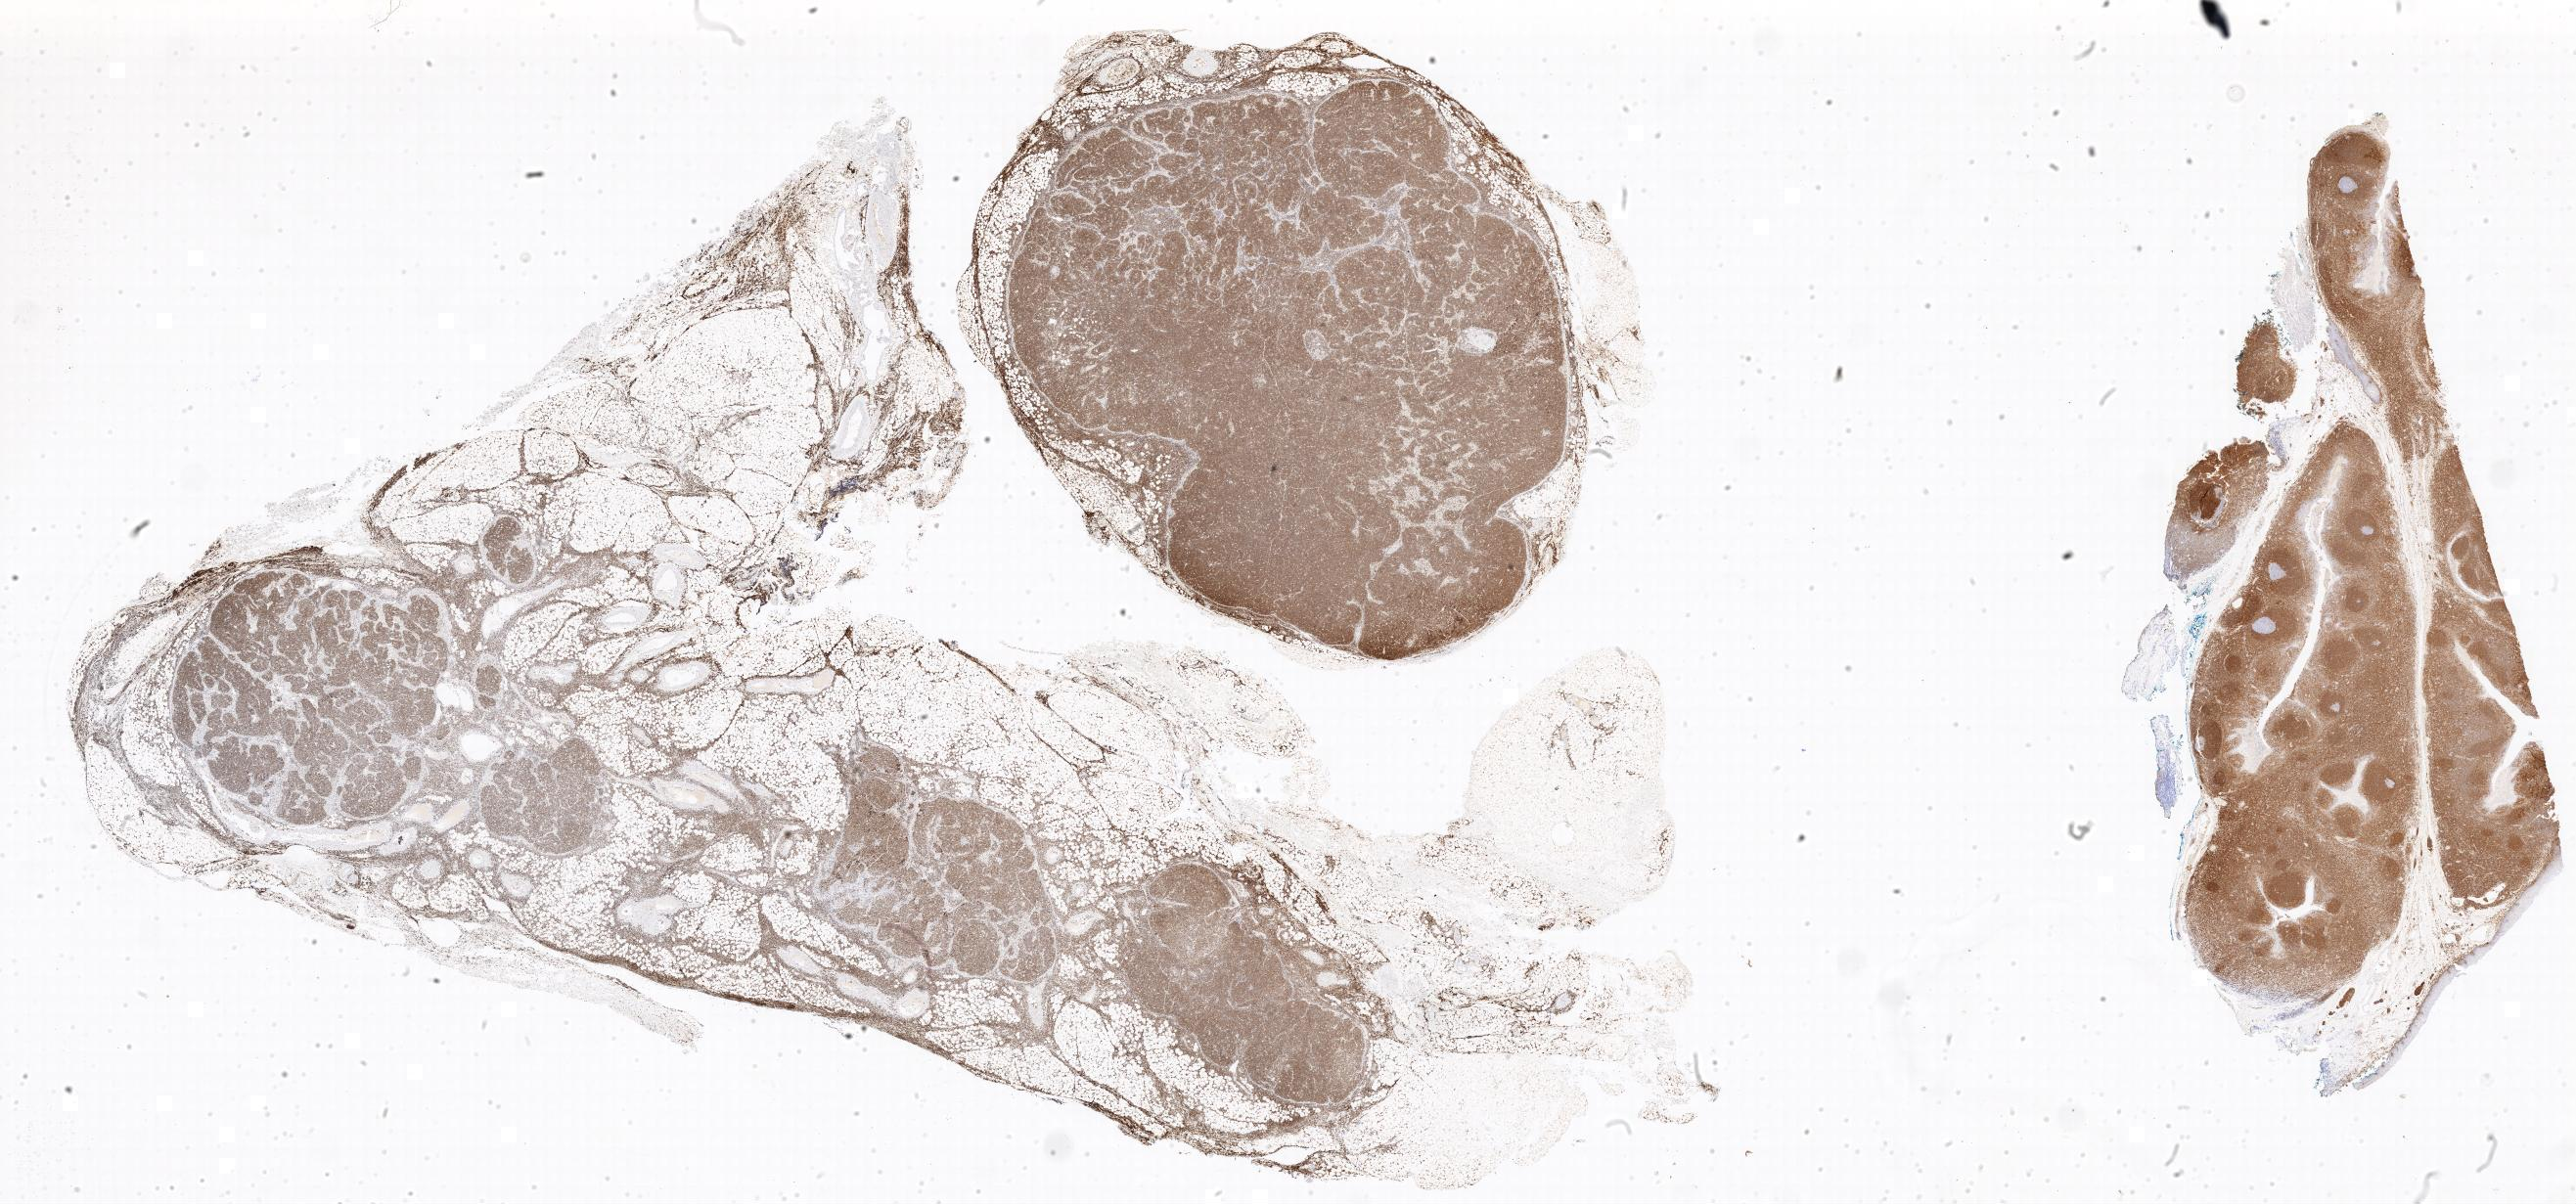
Immunohistochemistry (IHC) whole-slide image stained for BCL2 — a low-resolution overview of the entire scanned area; specimen: tumor tissue; site: spleen. Female patient, aged 15.
• diagnosis: Burkitt lymphoma, NOS